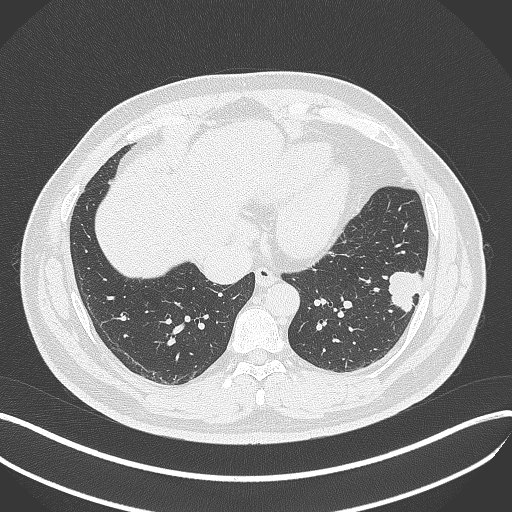
Chest CT, one axial slice; slice 134 of 429 in the series (ordered by position); 120 kVp; lung window (W 1500 / L -600 HU); 1 mm slice thickness; 512 × 512 image matrix, field of view 400 × 400 mm. Patient: male, 39 years. From the clinical record (not read from this slice): clinical TNM (as recorded): T2a N0 M0; histopathological grade: G2-3.
Annotated regions visible in this slice (rectangle marked by the reading radiologist):
- lung tumour (recorded histology: adenocarcinoma): box from (x=381, y=266) to (x=426, y=315) px